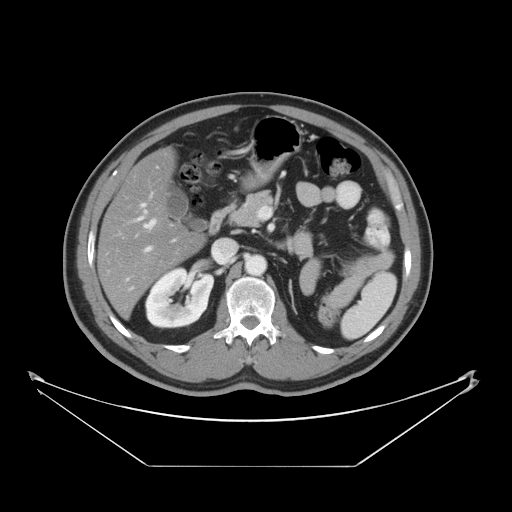
Contrast-enhanced abdominal CT, one axial slice. Position 22 of 46 along the scan axis. Intravenous contrast given. Soft-tissue window (W 400 / L 40 HU). 5 mm slice thickness. 512 × 512 image matrix, field of view 465 × 465 mm. Male patient, age 57 years. From the clinical record (not read from this slice): diagnosis: colorectal cancer liver metastases, imaged before liver resection; multiple liver metastases: no.
Outlined on this slice (manually delineated by an expert):
- hepatic veins: bounding box (x1, y1, x2, y2) in pixels: (139, 211, 155, 228)
- liver: (99, 150, 202, 315)
- planned liver remnant (the part of the liver to remain after resection): (99, 150, 202, 315)
- portal vein (with intrahepatic branches): (141, 204, 151, 251)